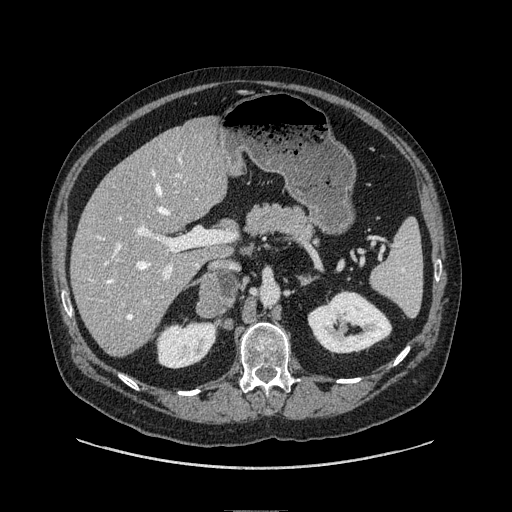
Contrast-enhanced abdominal CT, one axial slice; position 47 of 149 along the scan axis; soft-tissue window (W 400 / L 40 HU); 1.25 mm slice thickness; 512 × 512 image matrix. Male patient. From the clinical record (not read from this slice): diagnosis: adrenocortical carcinoma; tumour side: right adrenal; tumour size at pathology: 7.5 cm; Ki-67 index: 15 %; stage (as recorded): 2.
Annotated regions visible in this slice (semi-automatic segmentation, software-assisted and operator-edited):
- mass: bounding box [x1, y1, x2, y2] px = [198, 272, 237, 316]